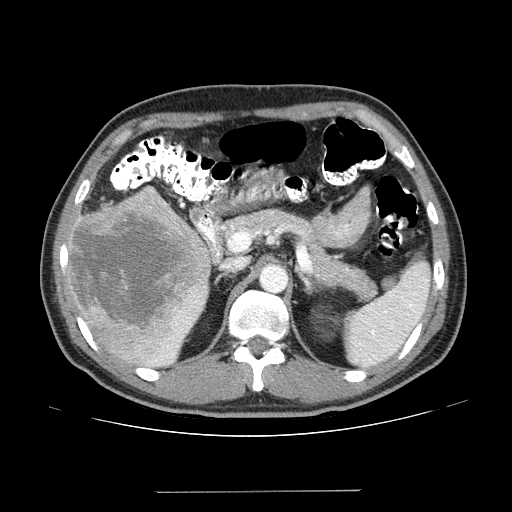
Contrast-enhanced abdominal CT (liver protocol), one axial slice; slice 78 of 131 in the series (ordered by position); reconstruction kernel STANDARD; one of 2 acquisitions stored at this slice position; soft-tissue window (W 400 / L 40 HU); 512 × 512 image matrix. From the clinical record (not read from this slice): diagnosis: hepatocellular carcinoma (patient treated with transarterial chemoembolisation; whether this scan precedes or follows treatment is not stated here); TNM stage (as recorded): Stage-I; Child-Pugh class: A; tumour differentiation: poorly differentiated; tumour size: 10.3 cm.
Outlined on this slice (semi-automatically segmented with operator editing):
- liver parenchyma outside the tumour (the mass and vessels are separate outlines, so this box may not span the whole liver): box from (x=64, y=186) to (x=210, y=366) px
- mass: (x=67, y=186)–(x=210, y=334)
- liver vessels: (x=155, y=317)–(x=188, y=362)